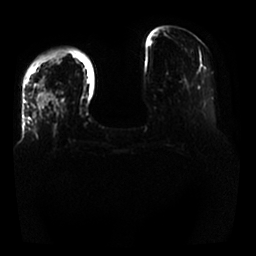
Breast MRI, one axial slice; slice 5 of 25 in the series (ordered by position); diffusion-weighted series; image 2 of 4 stored at this slice position (different b-values; order by instance number); 1.5 T; 256 × 256 image matrix, field of view 350 × 350 mm. Female patient.
Outlined on this slice (outlined manually by an expert reader):
- tumour on diffusion-weighted imaging: box from (x=38, y=90) to (x=53, y=106) px